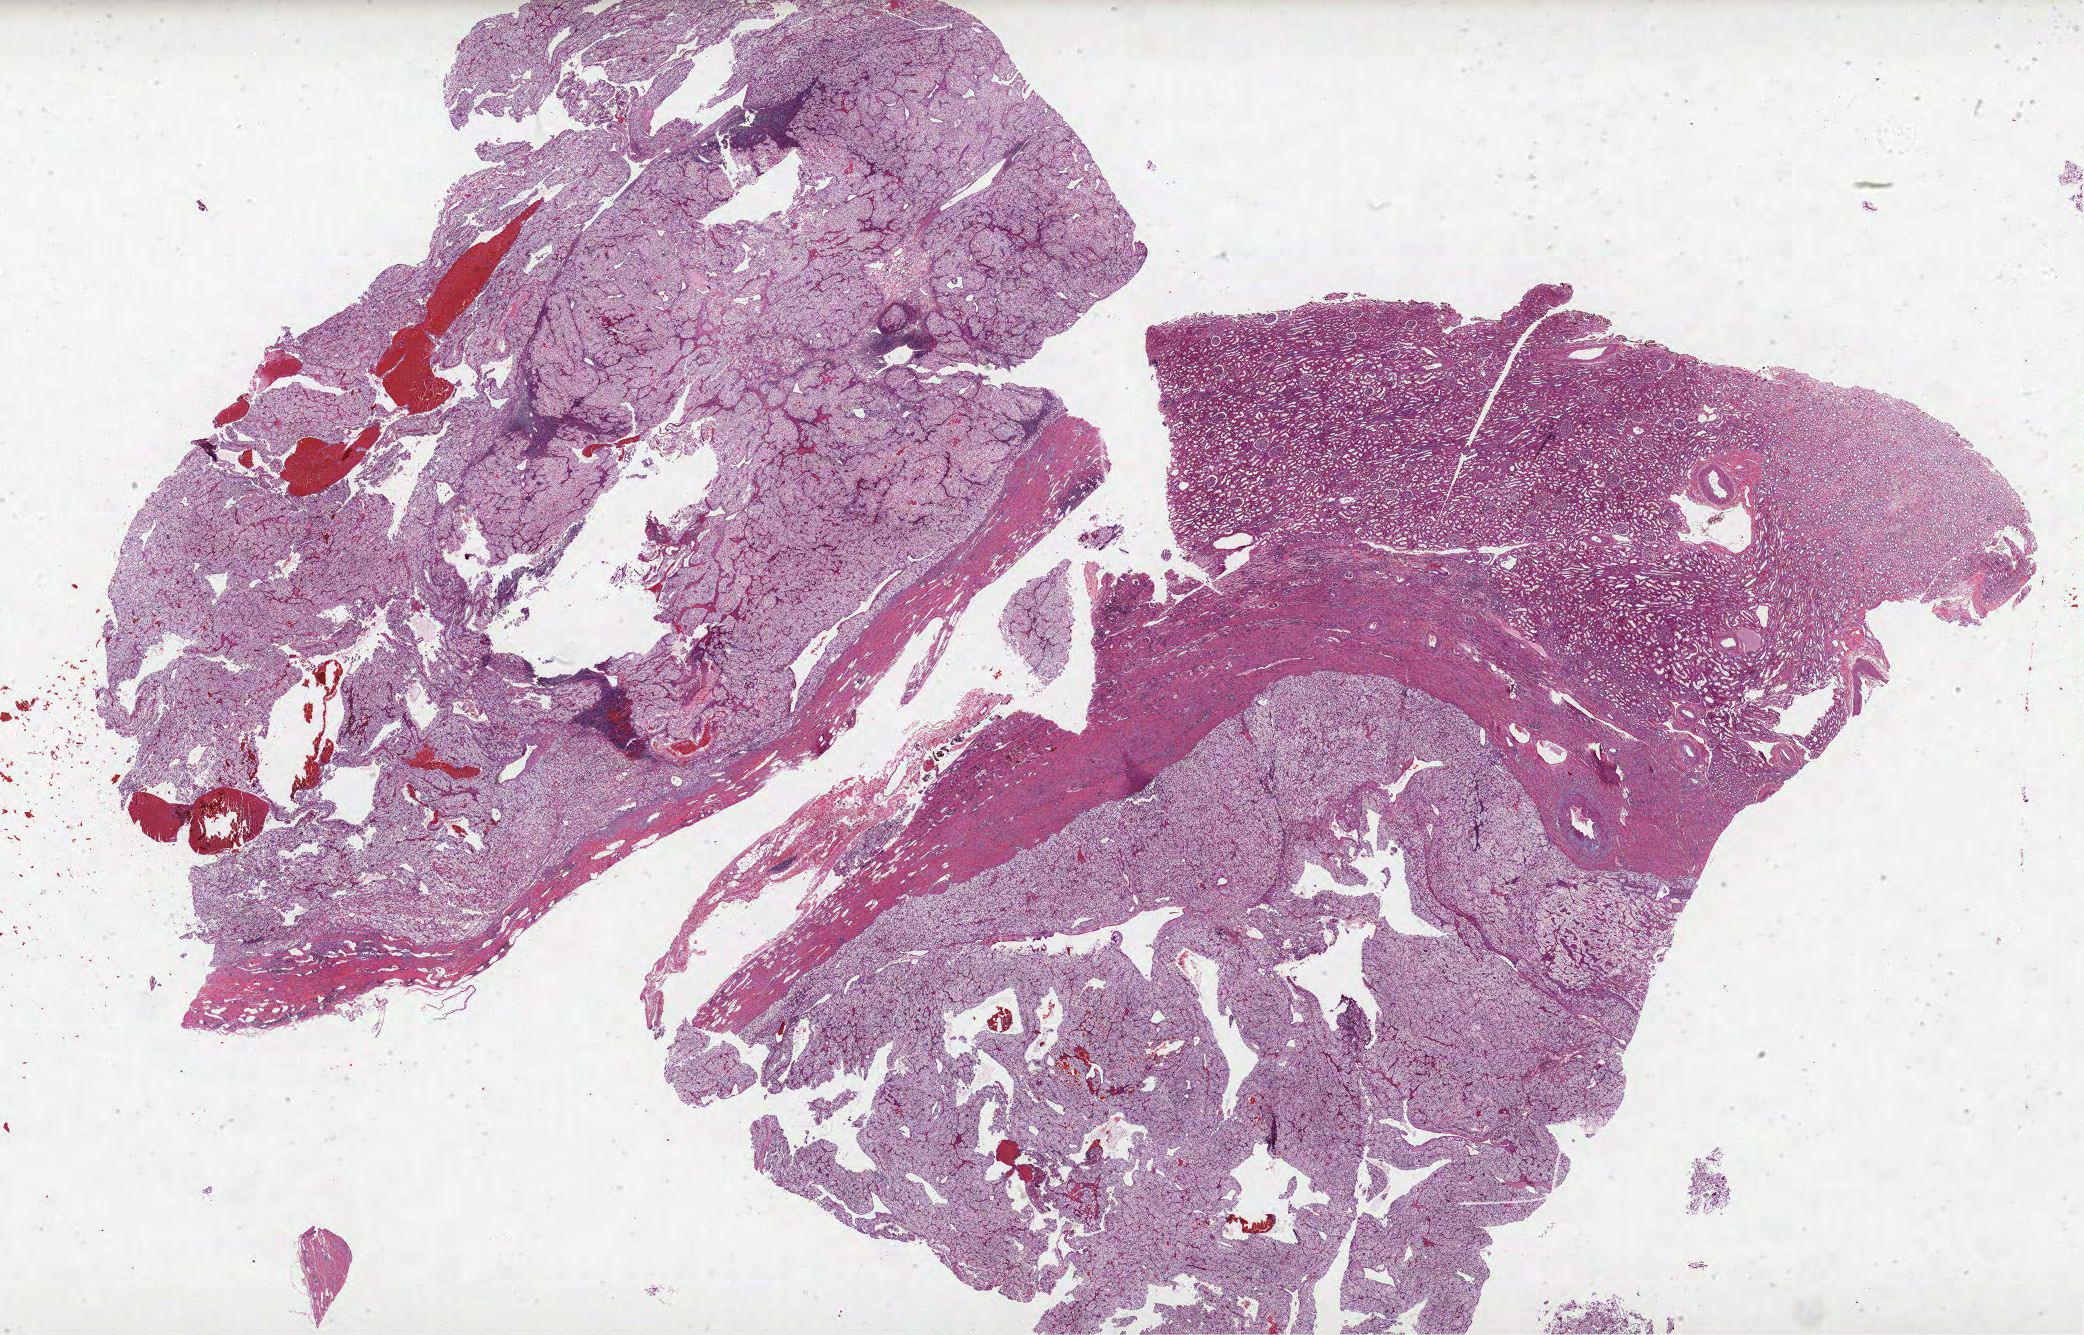
Digitized H&E tissue section (whole slide), shown as a low-resolution overview of the whole scanned area (about 33.3 x 21.3 mm); formalin-fixed paraffin-embedded (FFPE) diagnostic section; sample: primary tumour, kidney. Female patient; age at initial diagnosis 72 years. Histologic grade: G2 (moderately differentiated).
Histologic diagnosis: Clear cell adenocarcinoma, NOS. AJCC pathologic stage: I. Laterality: left.